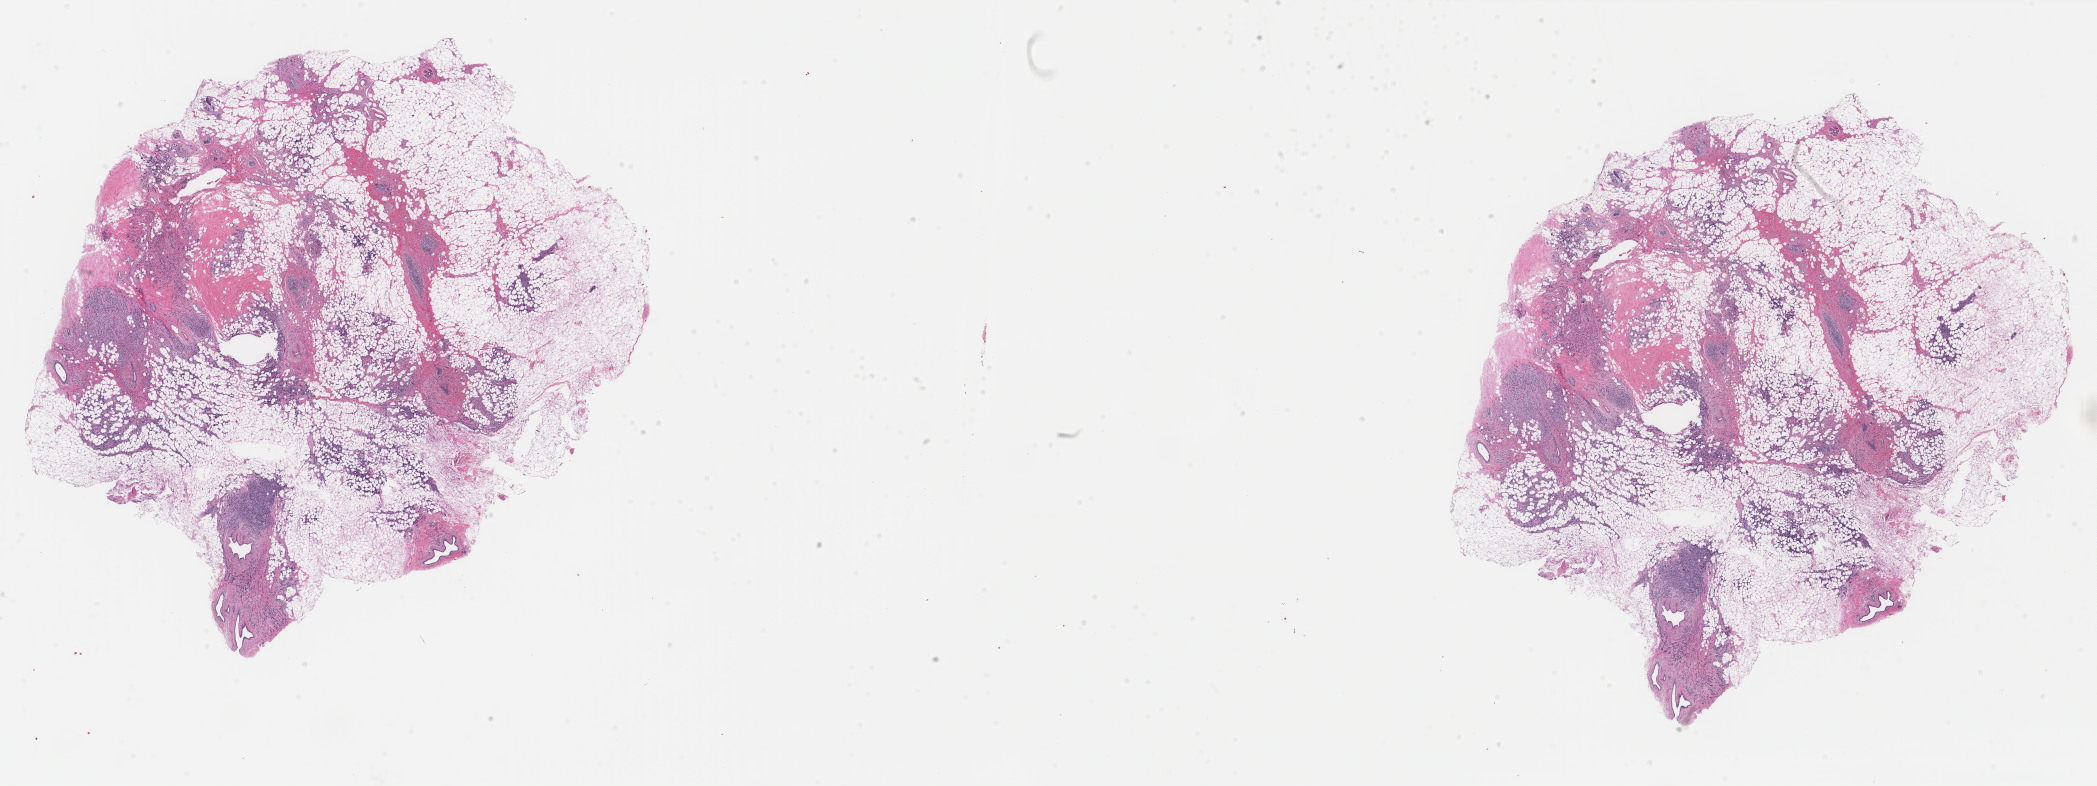
Digitized Hematoxylin and eosin (H&E) stained tissue section (whole slide) — low-resolution overview of the scanned area, about 33.3 x 12.5 mm; FFPE section; sample: primary tumour, breast. Female, age 55 years at initial diagnosis.
Pathologic diagnosis: Infiltrating duct carcinoma, NOS. AJCC pathologic stage: IA (7th edition). Lymph nodes positive (case pathology): 0 of 14 examined.